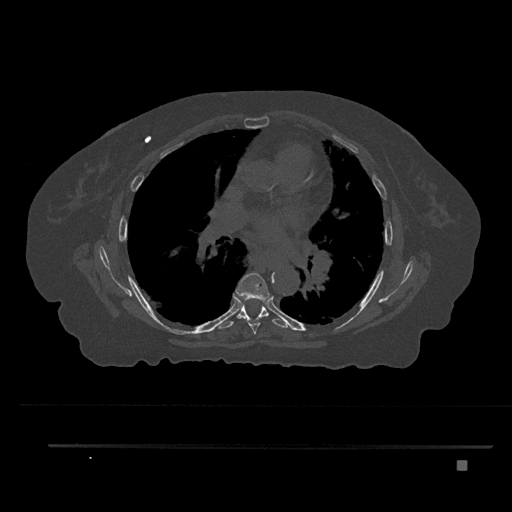
CT including the spine, one axial slice; slice 507 of 797 in the series (ordered by position); bone window (W 1800 / L 400 HU); 0.5 mm slice thickness; 512 × 512 image matrix, field of view 437 × 437 mm. Patient: female, 76 years. From the clinical record (not read from this slice): primary cancer: lung; vertebrae with lytic lesions (as recorded): T11, L3.
Annotated regions visible in this slice (semi-automatic segmentation, software-assisted and operator-edited):
- T6 vertebra: box from (x=234, y=273) to (x=270, y=335) px
- T7 vertebra: (x=218, y=303)–(x=289, y=329)